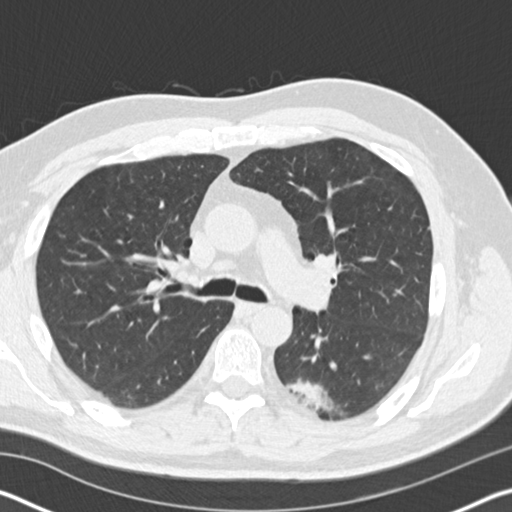
Low-dose screening chest CT, one axial slice. Position 110 of 178 along the scan axis. Reconstruction kernel B30f. 120 kVp. Lung window (W 1500 / L -600 HU). 512 × 512 image matrix, field of view 340 × 340 mm.
Outlined on this slice (outlined manually by an expert reader):
- lesion 1 (tumor, lower lobe of left lung): bounding box (x1, y1, x2, y2) in pixels: (286, 378, 334, 412)